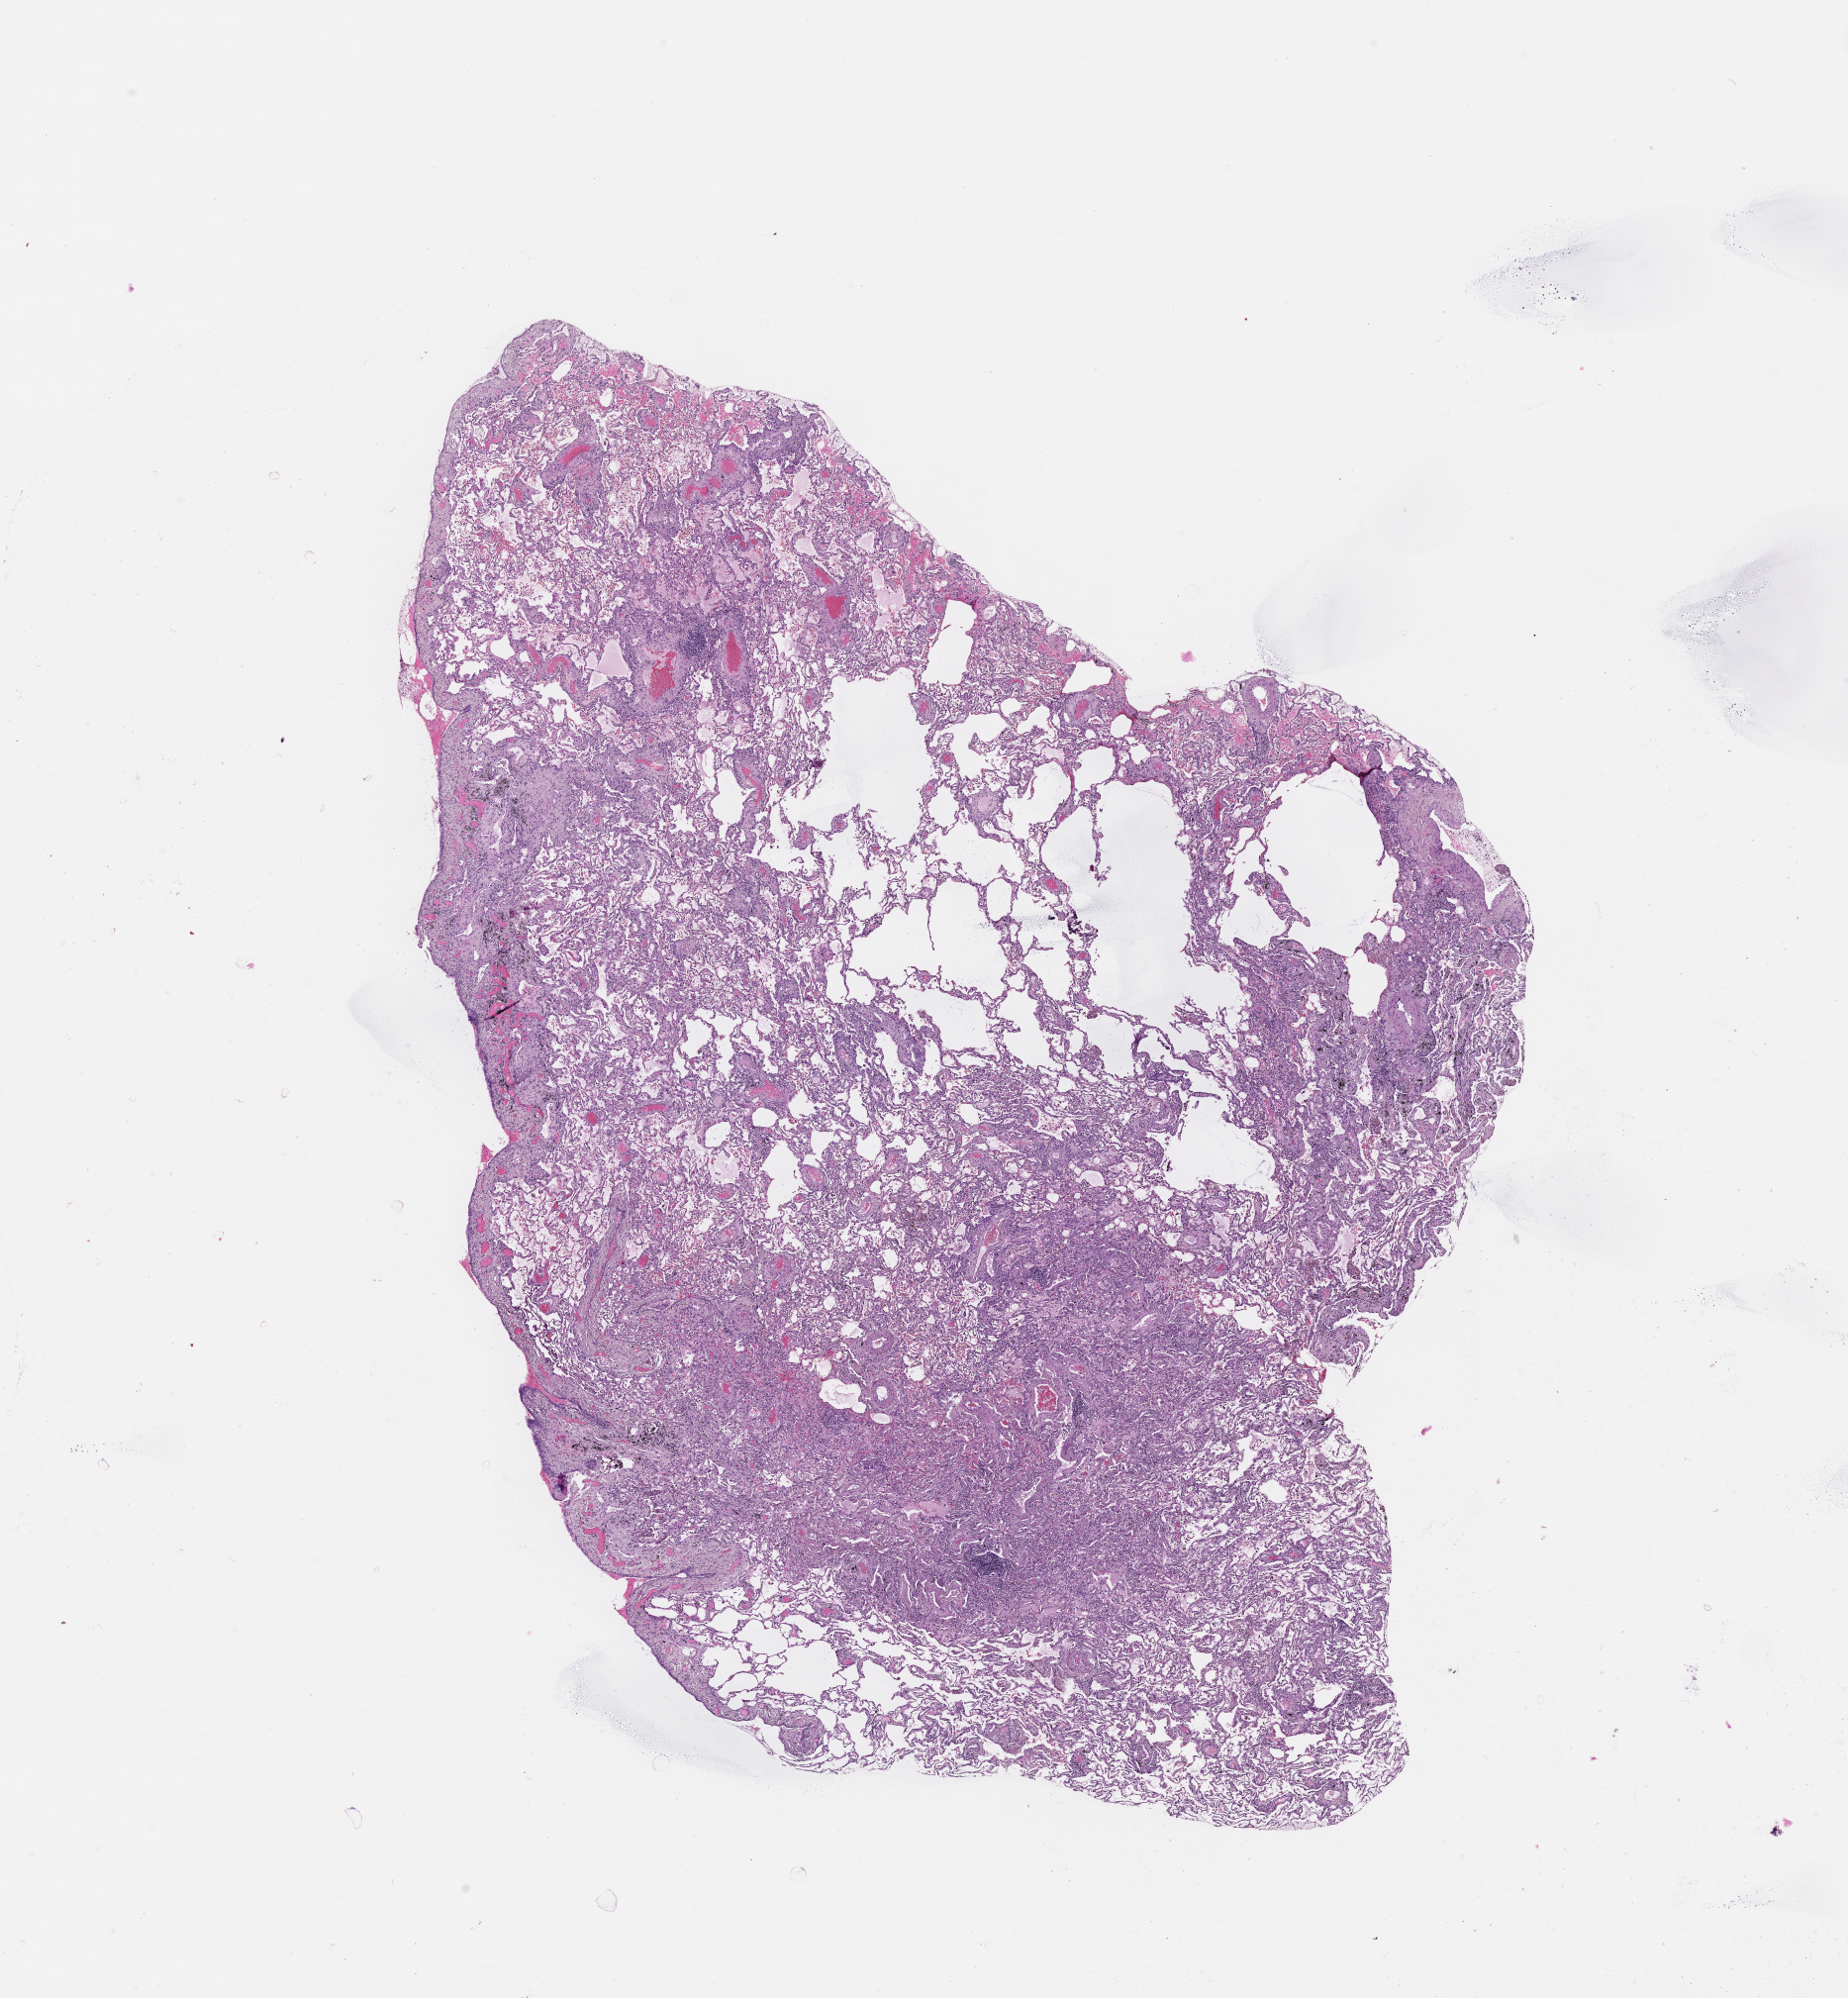
Whole-slide histology image, H&E, low-resolution overview of the scanned area, about 15.0 x 16.2 mm (from a 20x scan). Lung, tissue type not recorded.
- patient diagnosis (cohort enrolment): squamous cell carcinoma (lung)